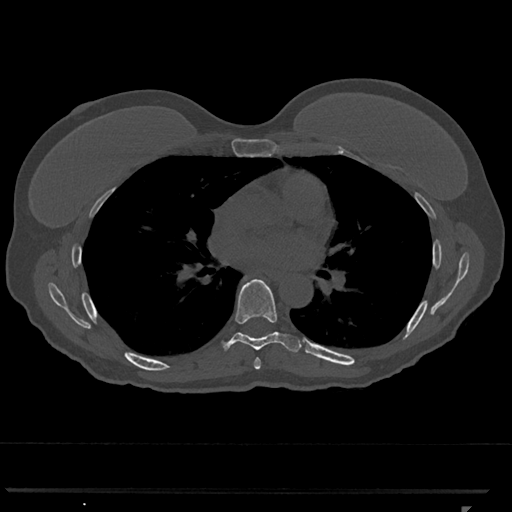
CT including the spine, one axial slice. Slice 712 of 793 in the series (ordered by position). Reconstruction kernel Br40s/3. 120 kVp. Bone window (W 1800 / L 400 HU). 0.5 mm slice thickness. 512 × 512 image matrix. Female patient, age 62 years. From the clinical record (not read from this slice): primary cancer: renal.
Outlined on this slice (semi-automatic segmentation, software-assisted and operator-edited):
- T6 vertebra: bounding box [x1, y1, x2, y2] px = [254, 358, 261, 370]
- T7 vertebra: [220, 279, 302, 352]